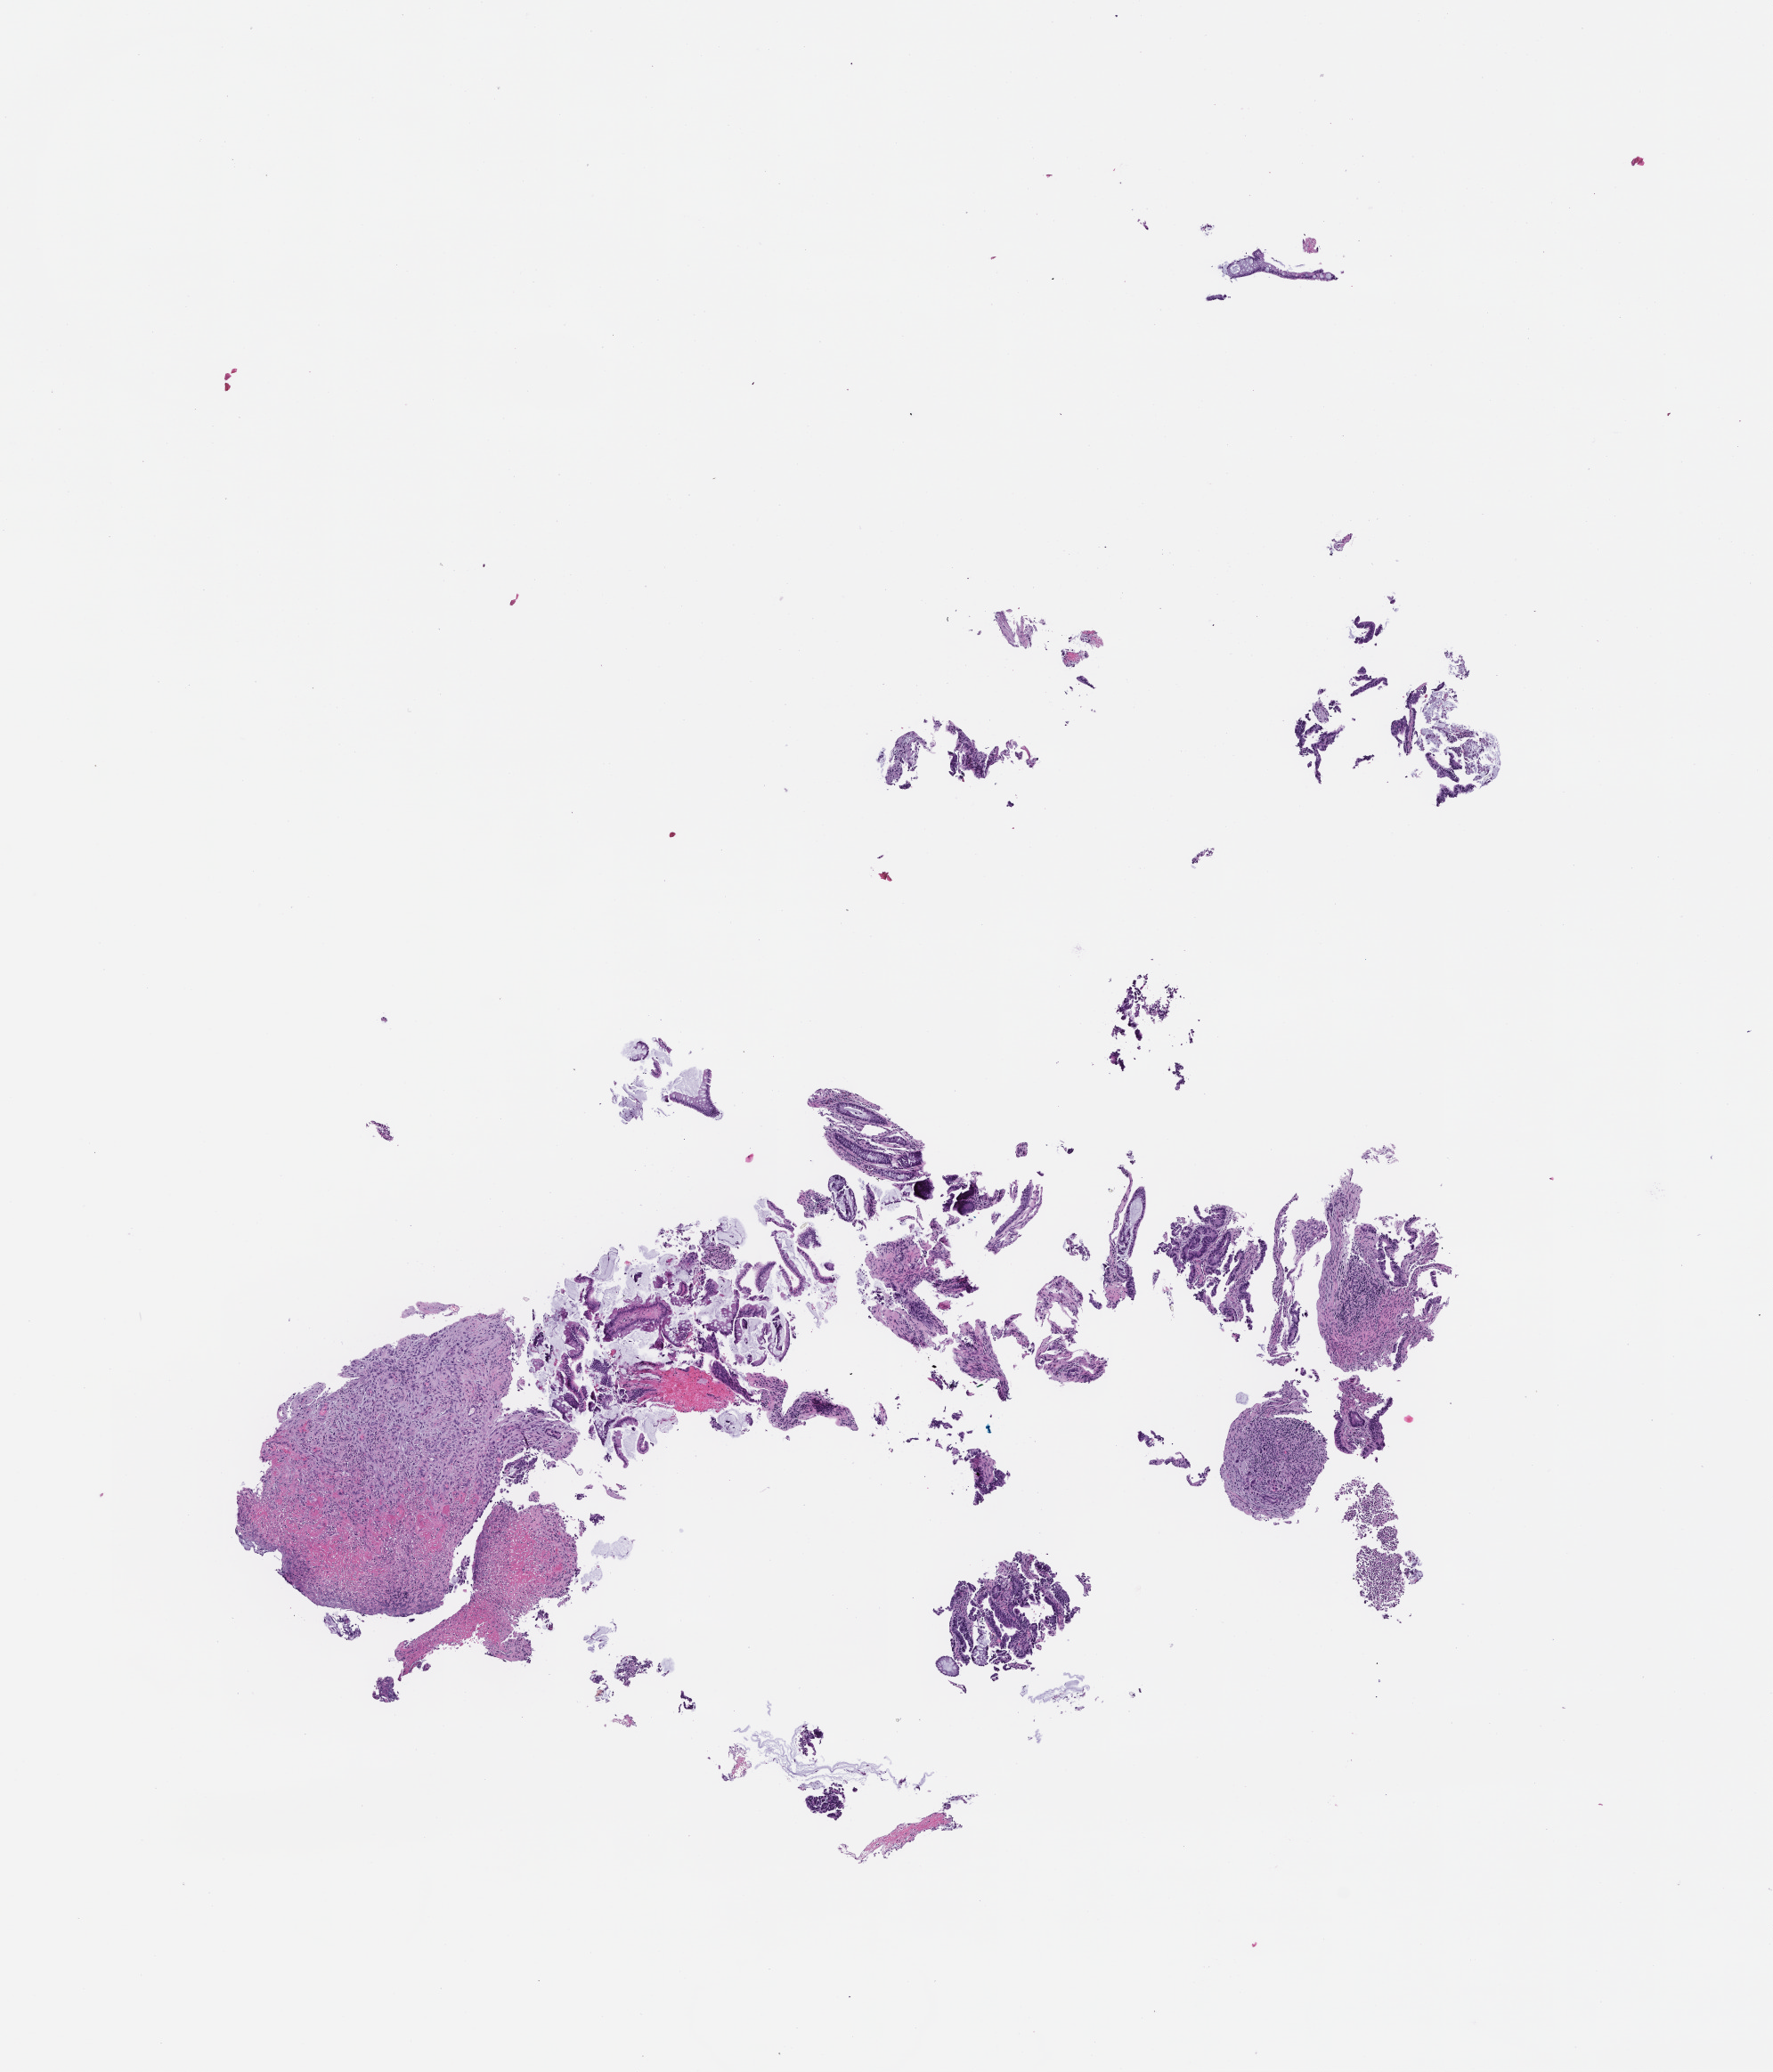
H&E whole-slide image, shown as a low-resolution overview of the whole scanned area (about 8.0 x 9.4 mm), formalin-fixed paraffin-embedded section, site: rectum, archival tissue. Patient: male.
- this section: primary tumor
- diagnosis: Colorectal Carcinoma